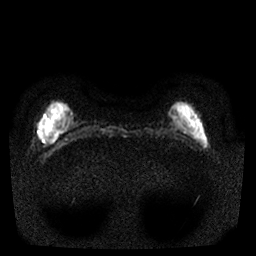
Breast MRI, one axial slice; slice 1 of 25 in the series (ordered by position); diffusion-weighted series; image 2 of 4 stored at this slice position (different b-values; order by instance number); 1.5 T; 4 mm slice thickness; 256 × 256 image matrix. Female patient.
Structures marked on this image (expert manual segmentation):
- tumour on diffusion-weighted imaging: bounding box <53,130,61,140> (left, top, right, bottom; pixels)